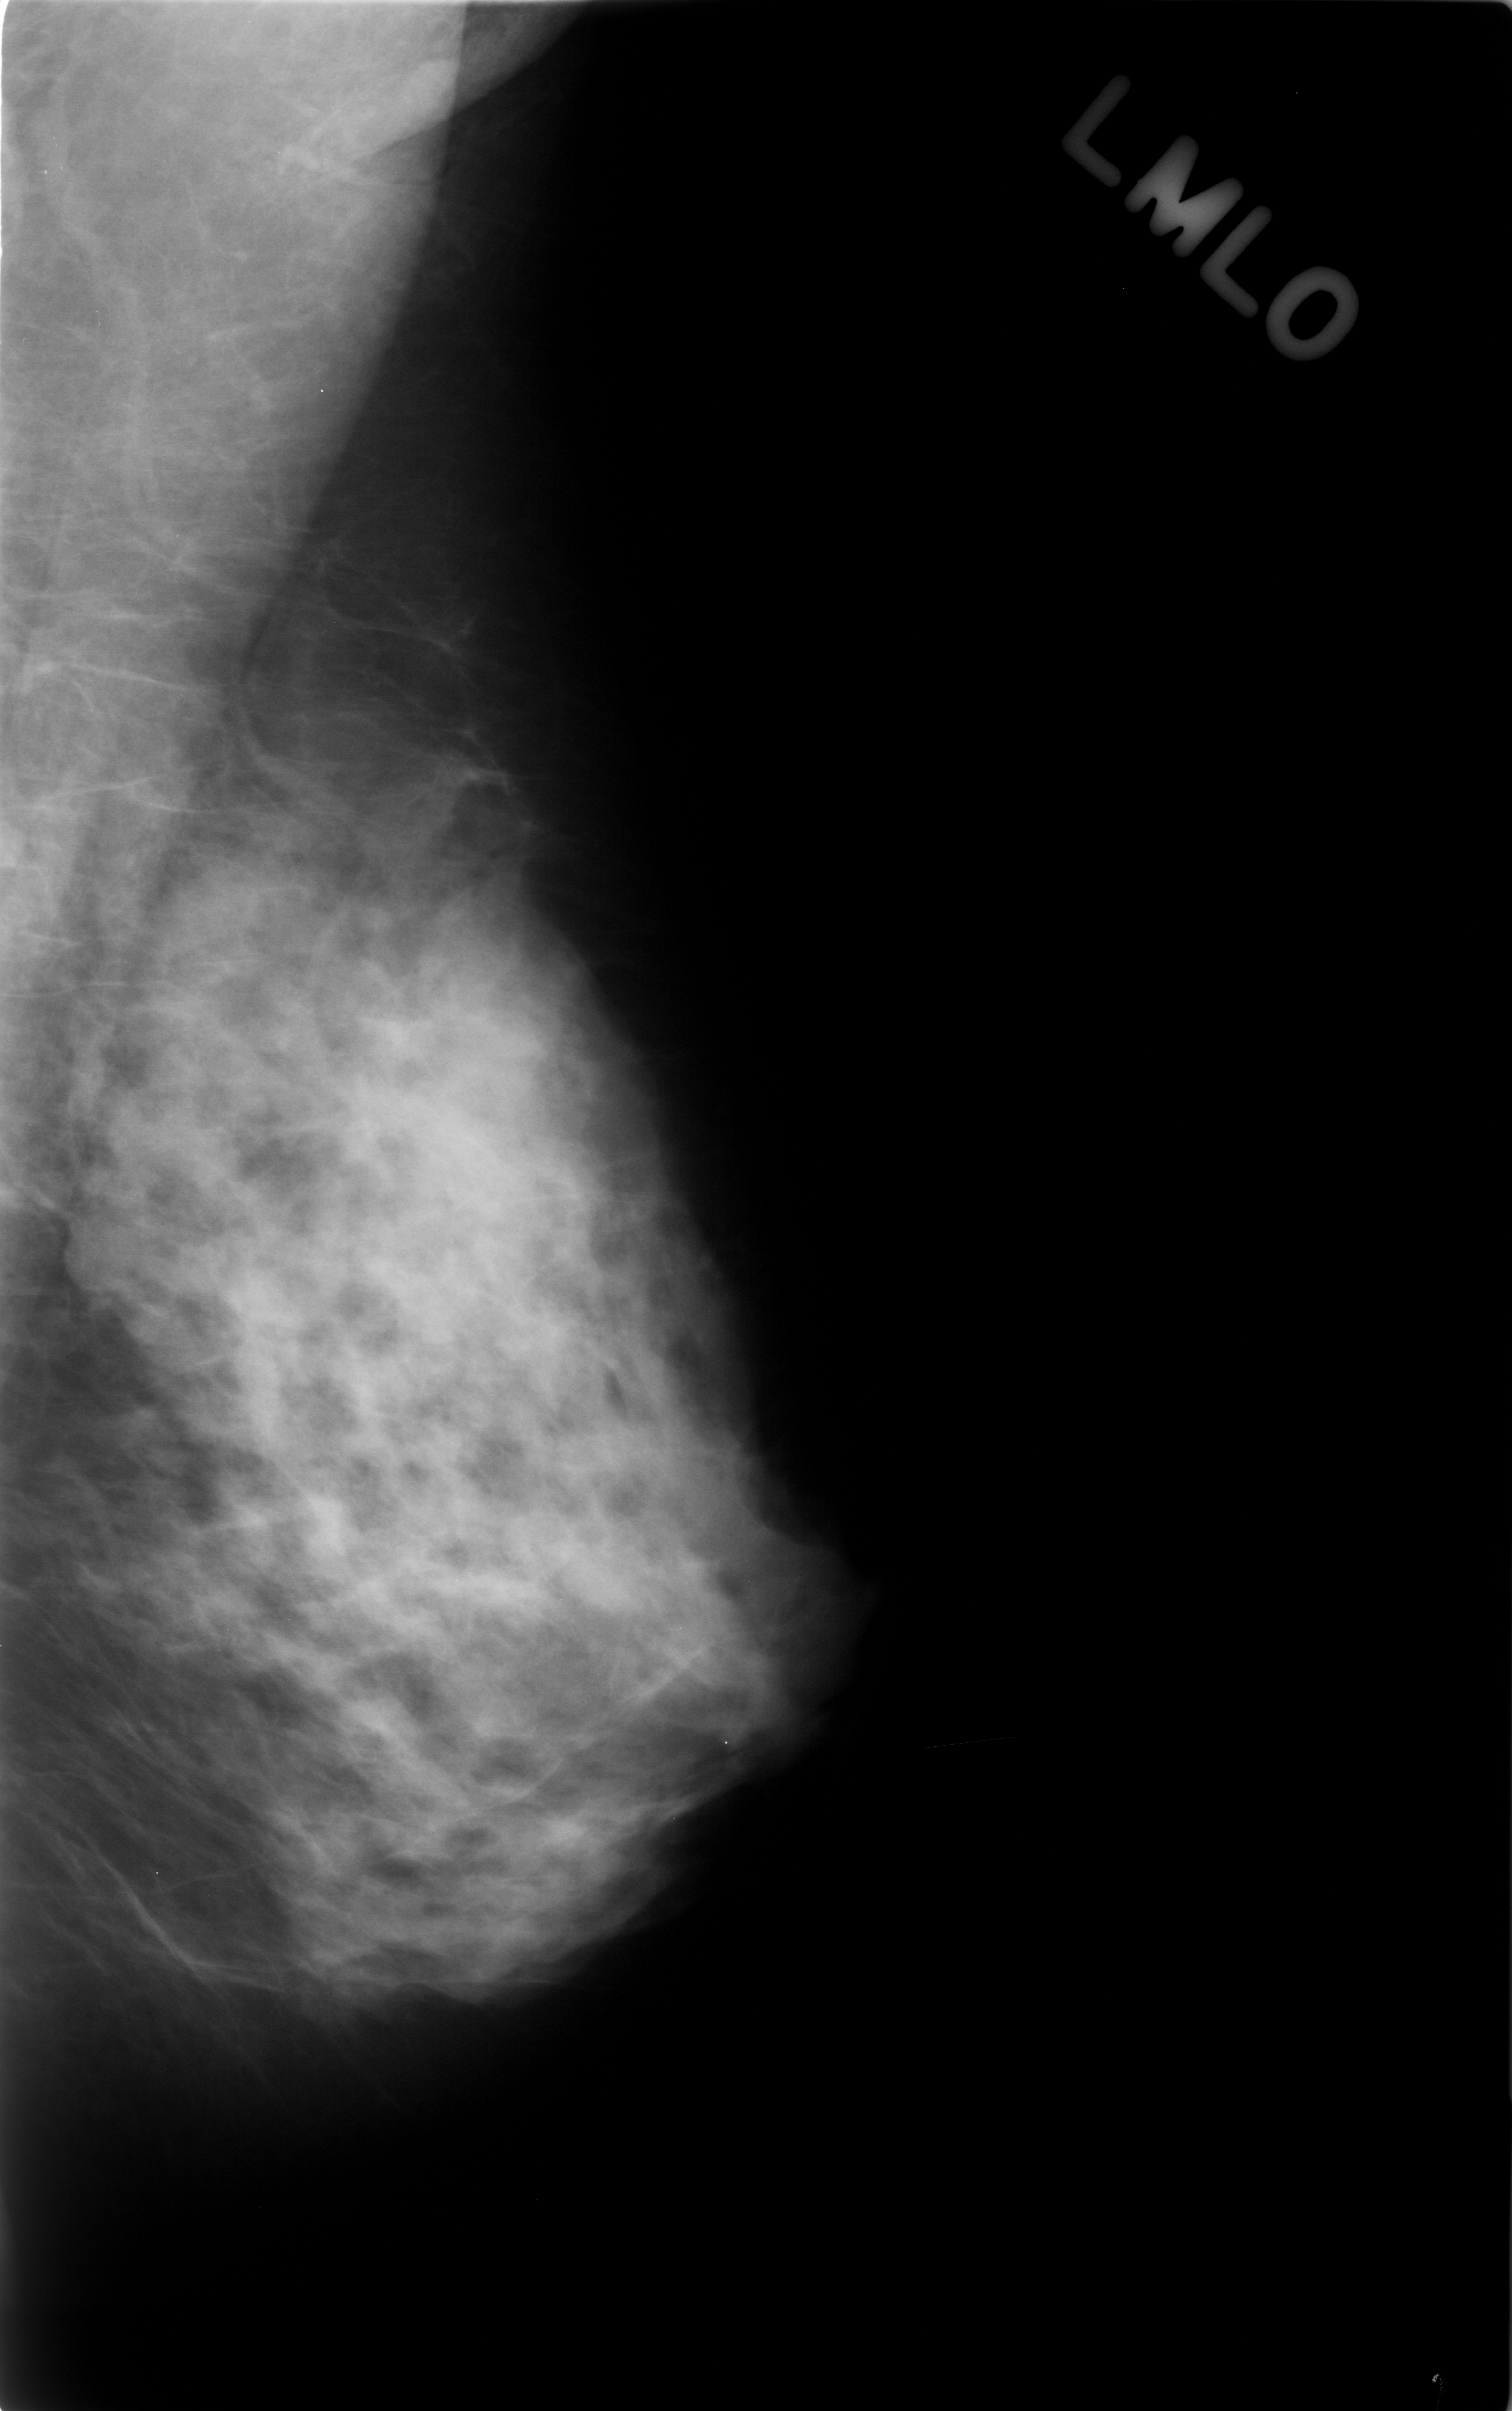
Scanned film-screen mammogram, left breast, MLO view, breast composition: heterogeneously dense (BI-RADS density category 3 of 4).
Finding: mass, shape round, margins microlobulated; BI-RADS assessment category 3; subtlety rating 3 on a 1 (subtle) to 5 (obvious) scale; benign; no additional work-up was recommended (benign without callback).